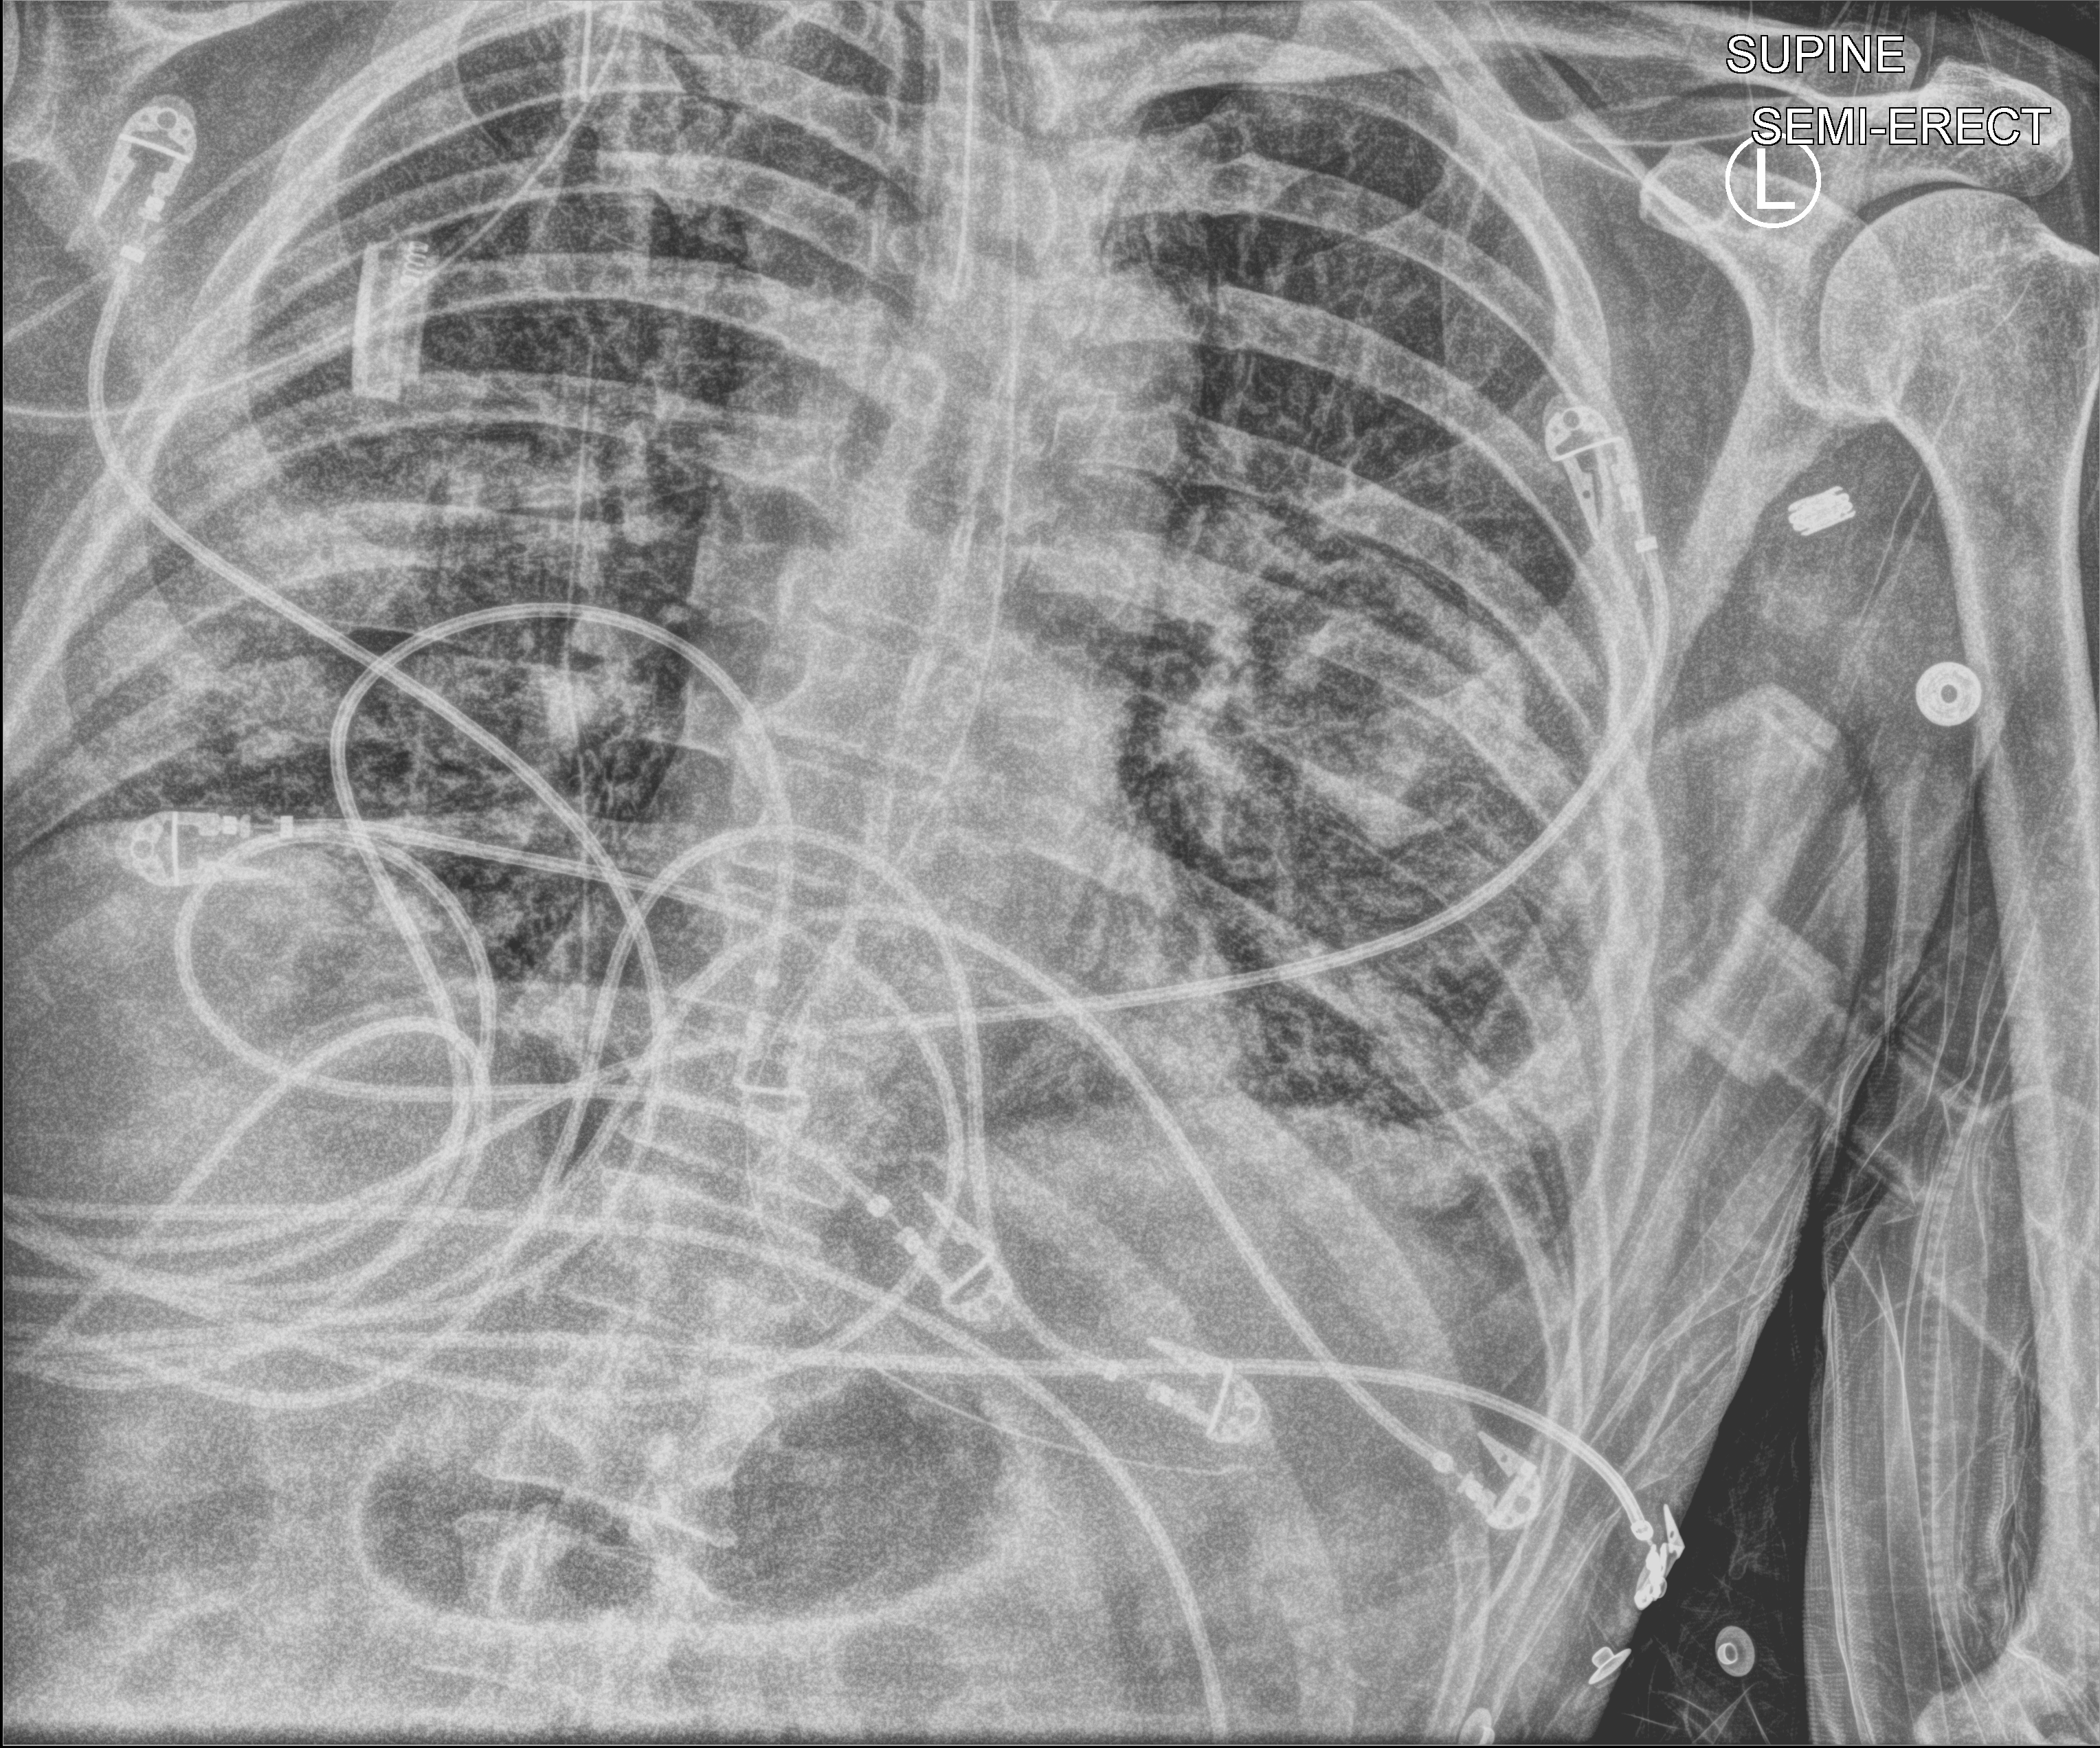
Bedside chest radiograph (computed radiography); anteroposterior (AP) projection. Patient hospitalised with COVID-19; male, aged 60–74 years.
Hospital-stay facts (about this admission, not read from this image; timing relative to this image not recorded):
- mechanically ventilated during this hospital stay: yes